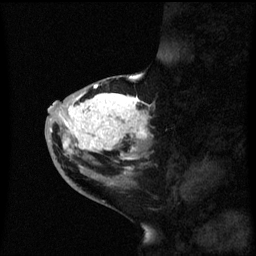
Breast MRI (dynamic contrast-enhanced), one sagittal slice. Position 25 of 60 along the scan axis. Dynamic contrast-enhanced series, image 2 of 3 at this slice position (ordered by acquisition). 1.5 T. TE 4.2 ms, TR 8.4 ms. 2.3 mm slice thickness. 256 × 256 image matrix. Patient: female, 46 years. Case-level facts recorded for this patient, not image findings: setting: breast cancer imaged before/during neoadjuvant chemotherapy; receptor status: HER2-positive.
Outlined on this slice (semi-automatic segmentation, software-assisted and operator-edited):
- analysis volume of interest (the breast-tissue region the enhancement analysis was run in; not a lesion): bounding box <46,86,155,171> (left, top, right, bottom; pixels)
- tumour enhancement mask (voxels above the 70 % enhancement threshold inside the analysis volume of interest): <54,86,151,171>